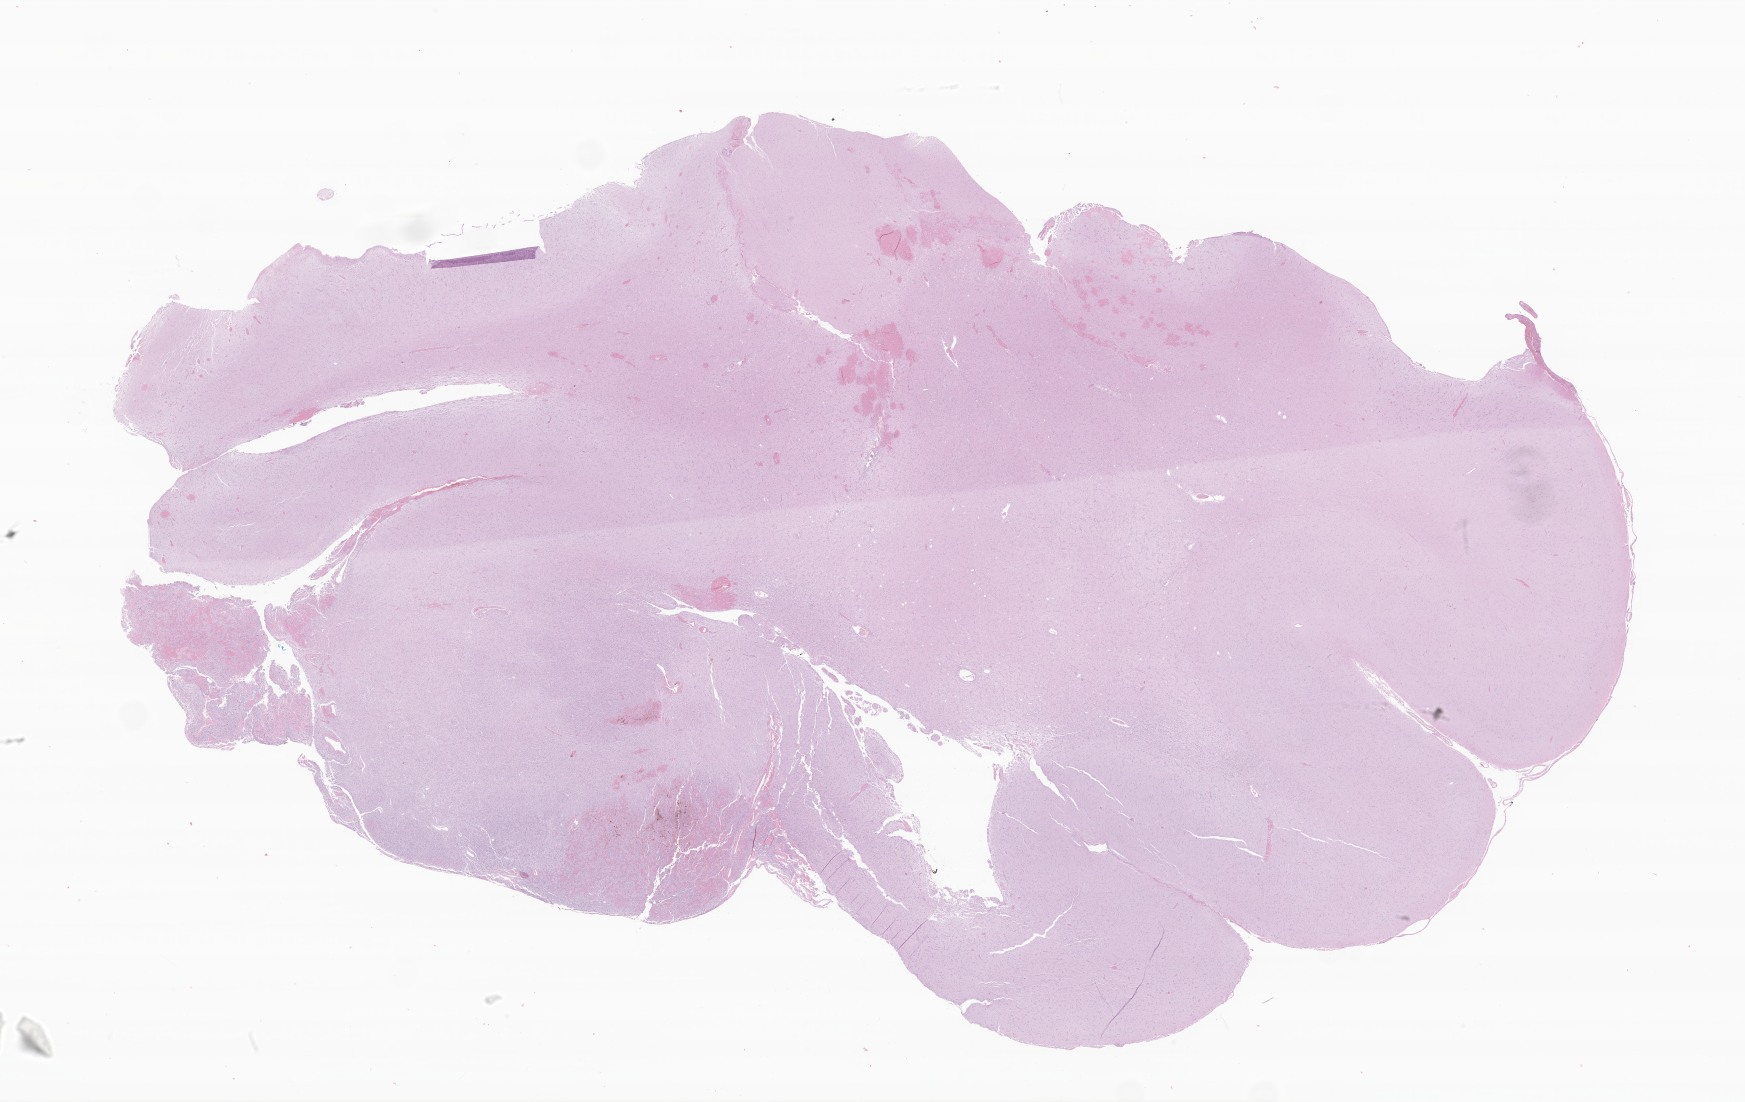
Digitized haematoxylin and eosin-stained section of tumor tissue from the temporal lobe, whole scanned area (about 29.4 x 18.6 mm) shown as a low-resolution overview; formalin-fixed paraffin-embedded section. Patient male; age 184 months (15 years 4 months).
Diagnosis: Pleomorphic xanthoastrocytoma, NOS.